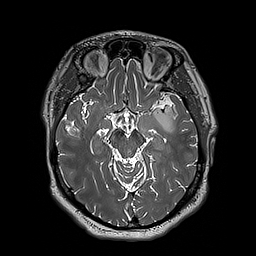
Brain MRI from a brain-tumour surgery series, one axial slice. Position 117 of 192 along the scan axis. 1 mm slice thickness. 256 × 256 image matrix, field of view 250 × 250 mm. From the clinical record (not read from this slice): histopathology: Astrocytoma; WHO grade: 3; IDH mutation: yes; tumour location: Left Insular.
Outlined on this slice (expert manual segmentation):
- tumour: bounding box (x1, y1, x2, y2) in pixels: (153, 105, 177, 132)